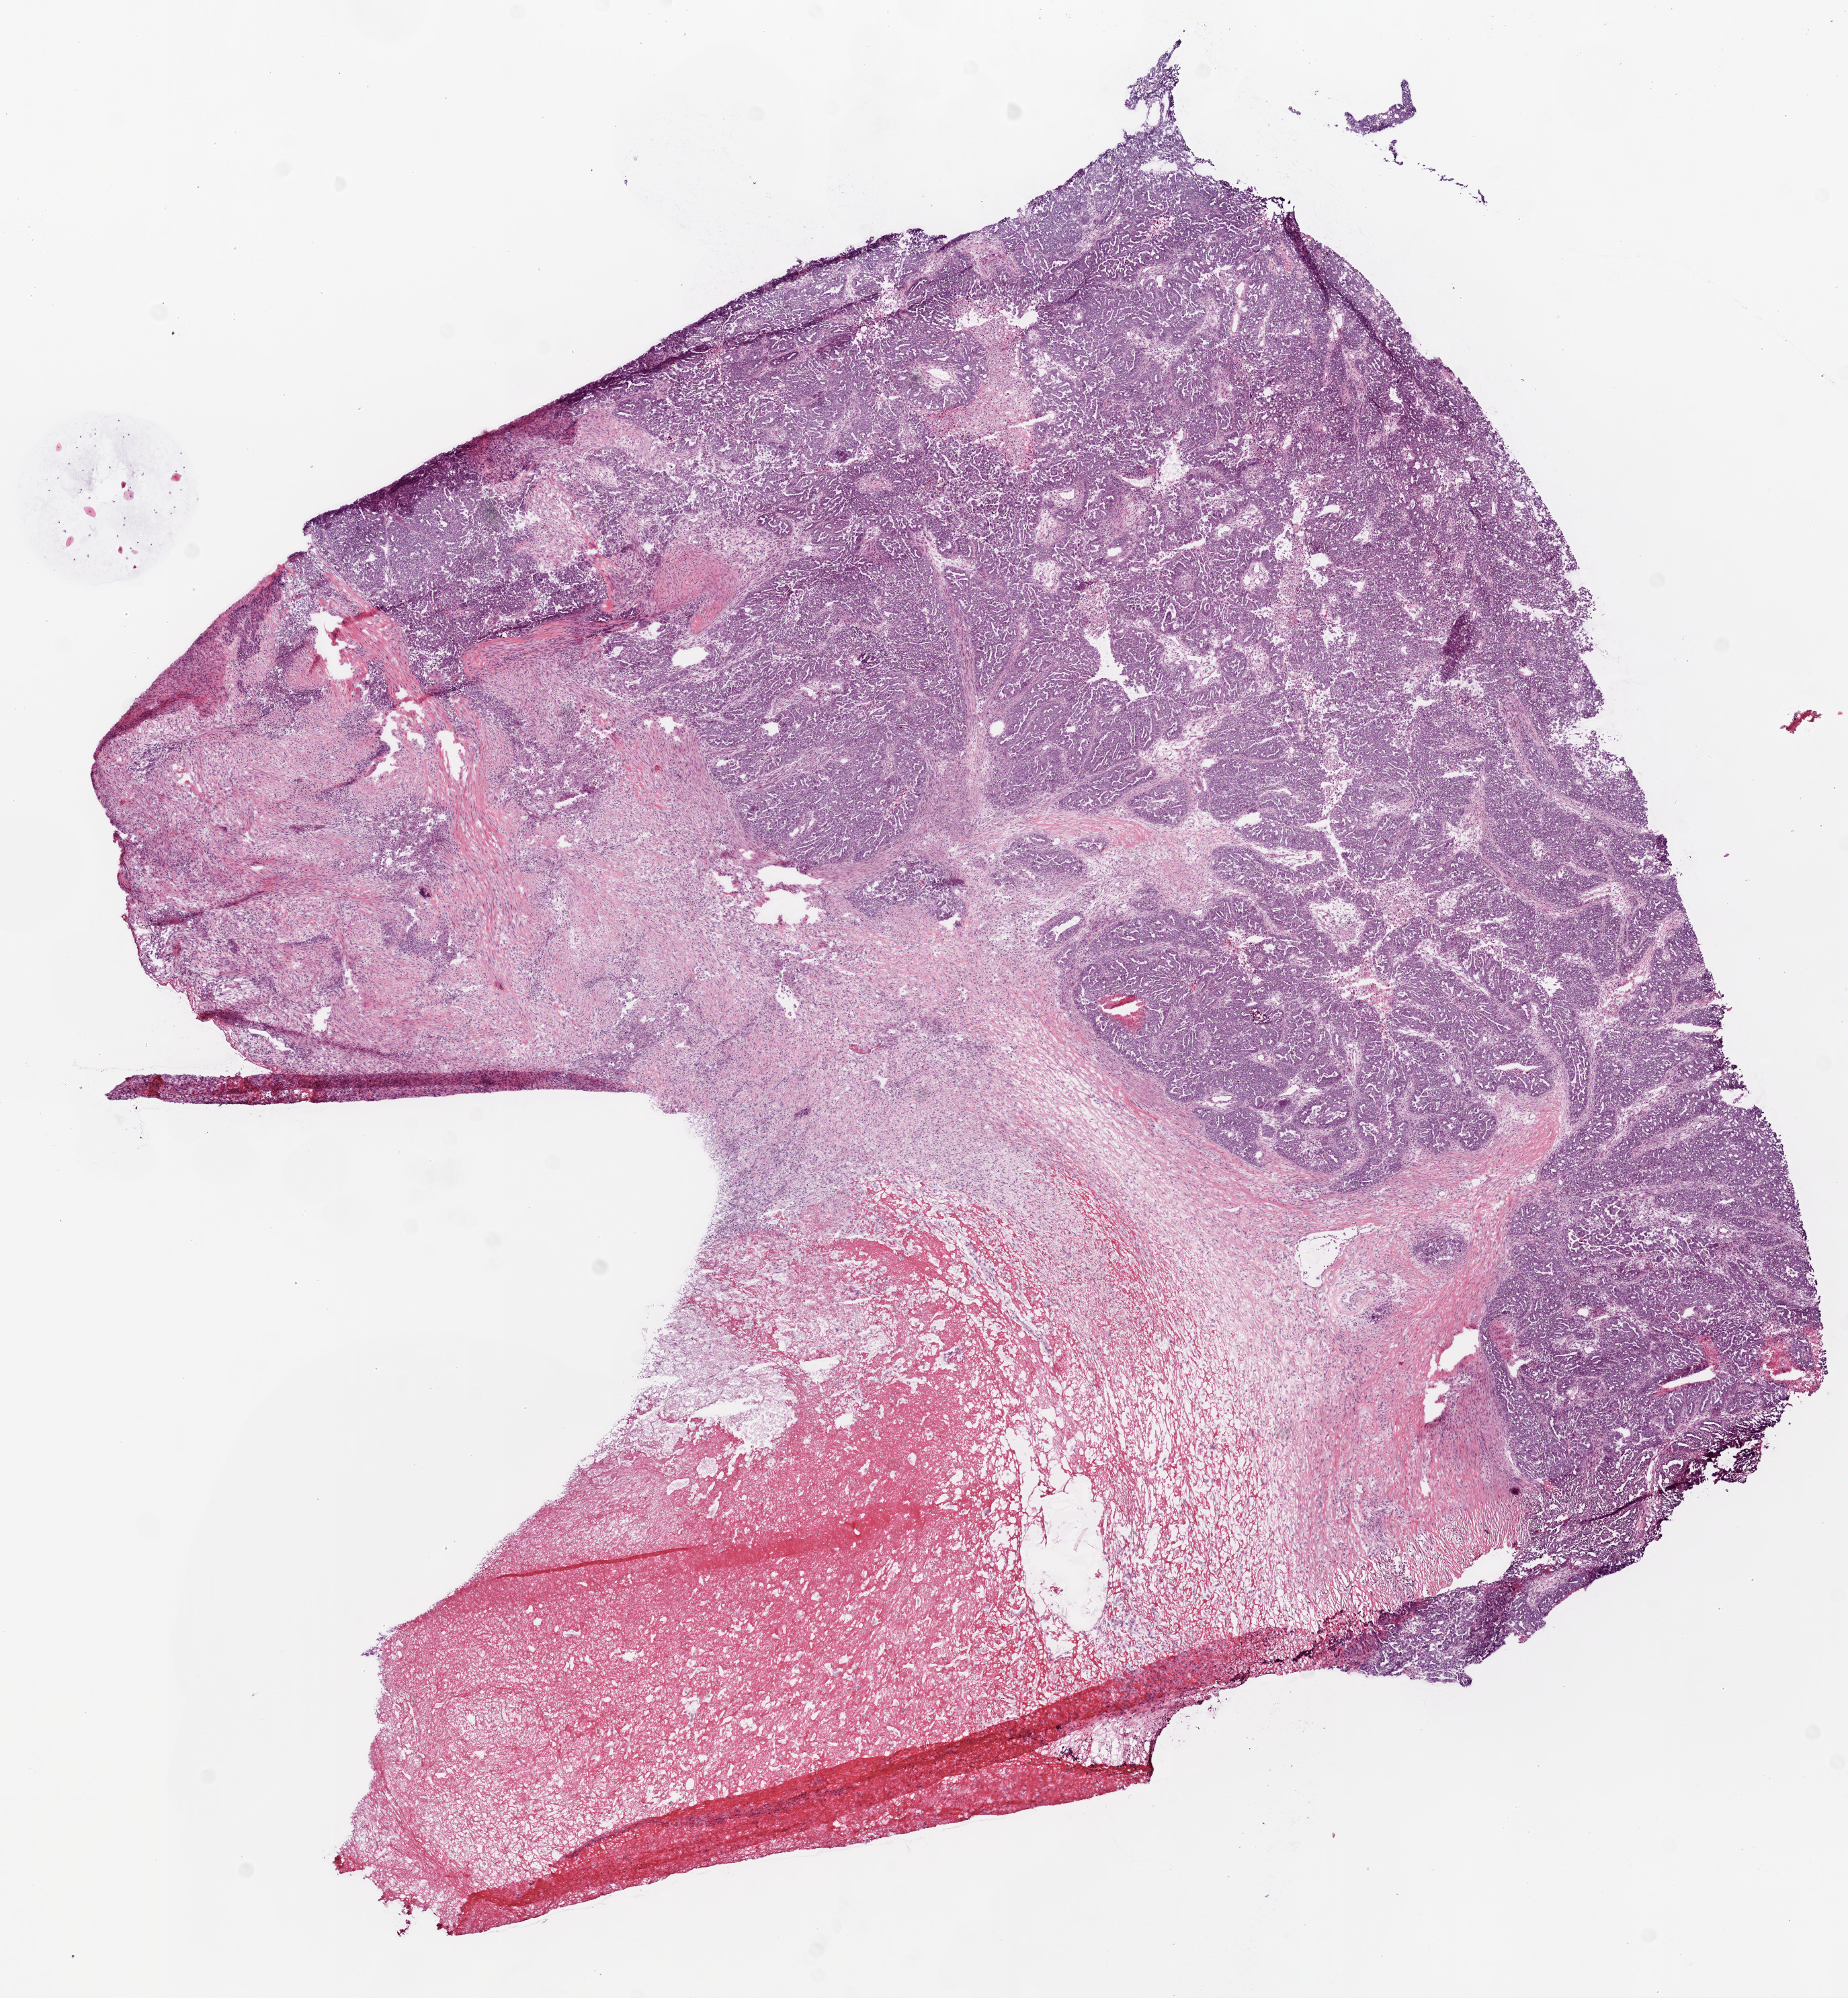
H&E-stained whole-slide image — whole scanned area (about 11.0 x 11.9 mm, from a 20x scan) shown as a low-resolution overview, frozen section, ovary, primary tumour sample. Female patient; age at initial diagnosis 30 years. Histologic grade: G3 (poorly differentiated). Composition of this section per pathologist review: tumour cells 55%, tumour nuclei 85%, normal cells 0%, stromal cells 40%, necrosis 5%.
• FIGO stage: IIIC
• histologic diagnosis: Serous cystadenocarcinoma, NOS
• laterality: bilateral